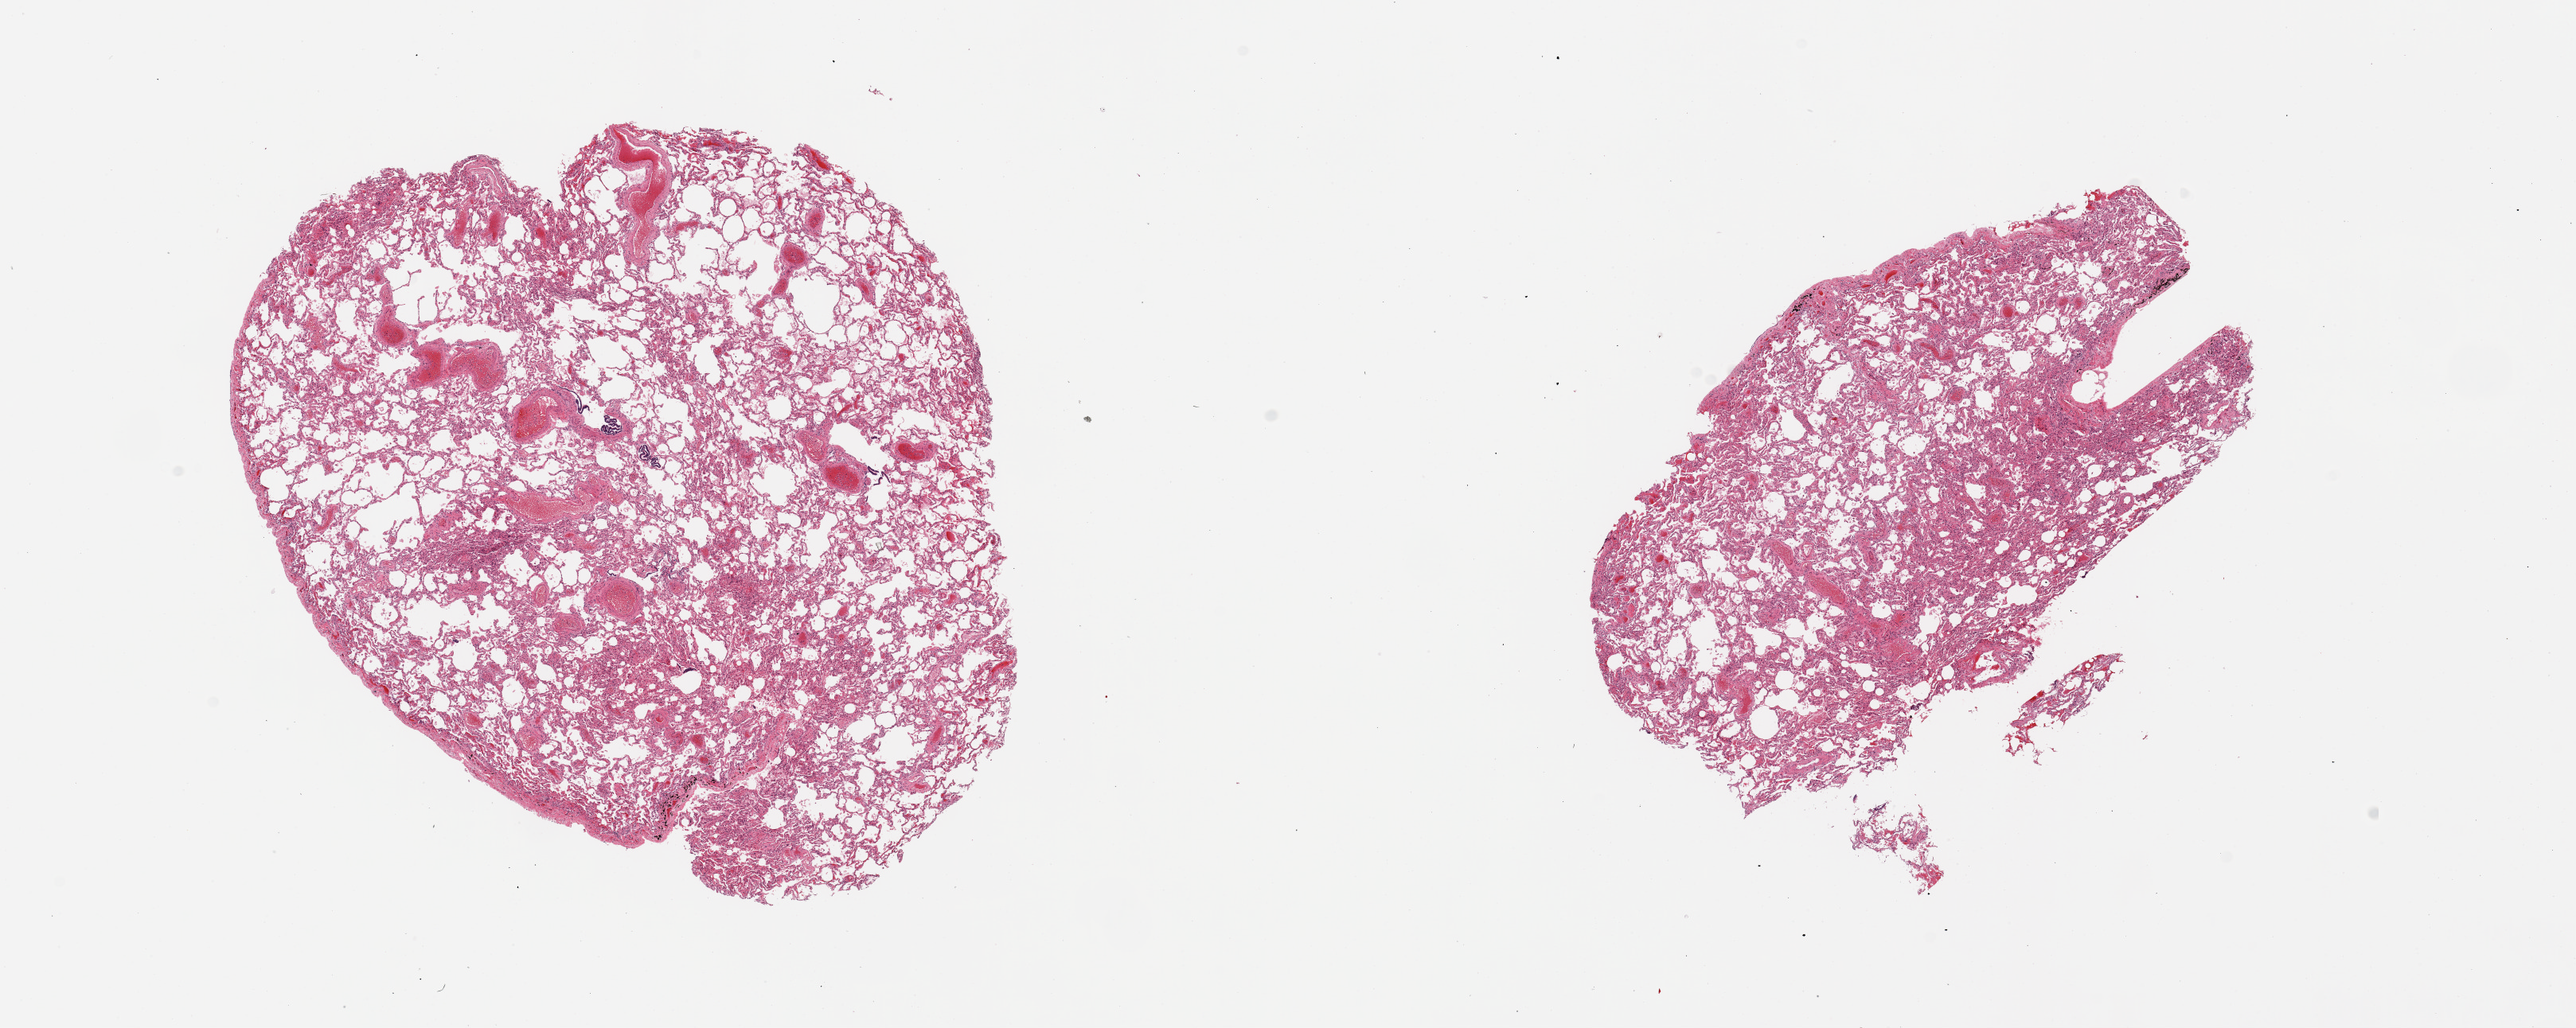
Digitized H&E-stained section — whole scanned area (about 25.6 x 10.2 mm) shown as a low-resolution overview. PAXgene-fixed paraffin-embedded (PFPE) section. Sampled site (target tissue): lung. Tissue donor sample. Donor: male.
Reviewer comment on this tissue sample: 2 pieces; includes pleura (target is 1 cm below pleura), some mild emphysematous change.